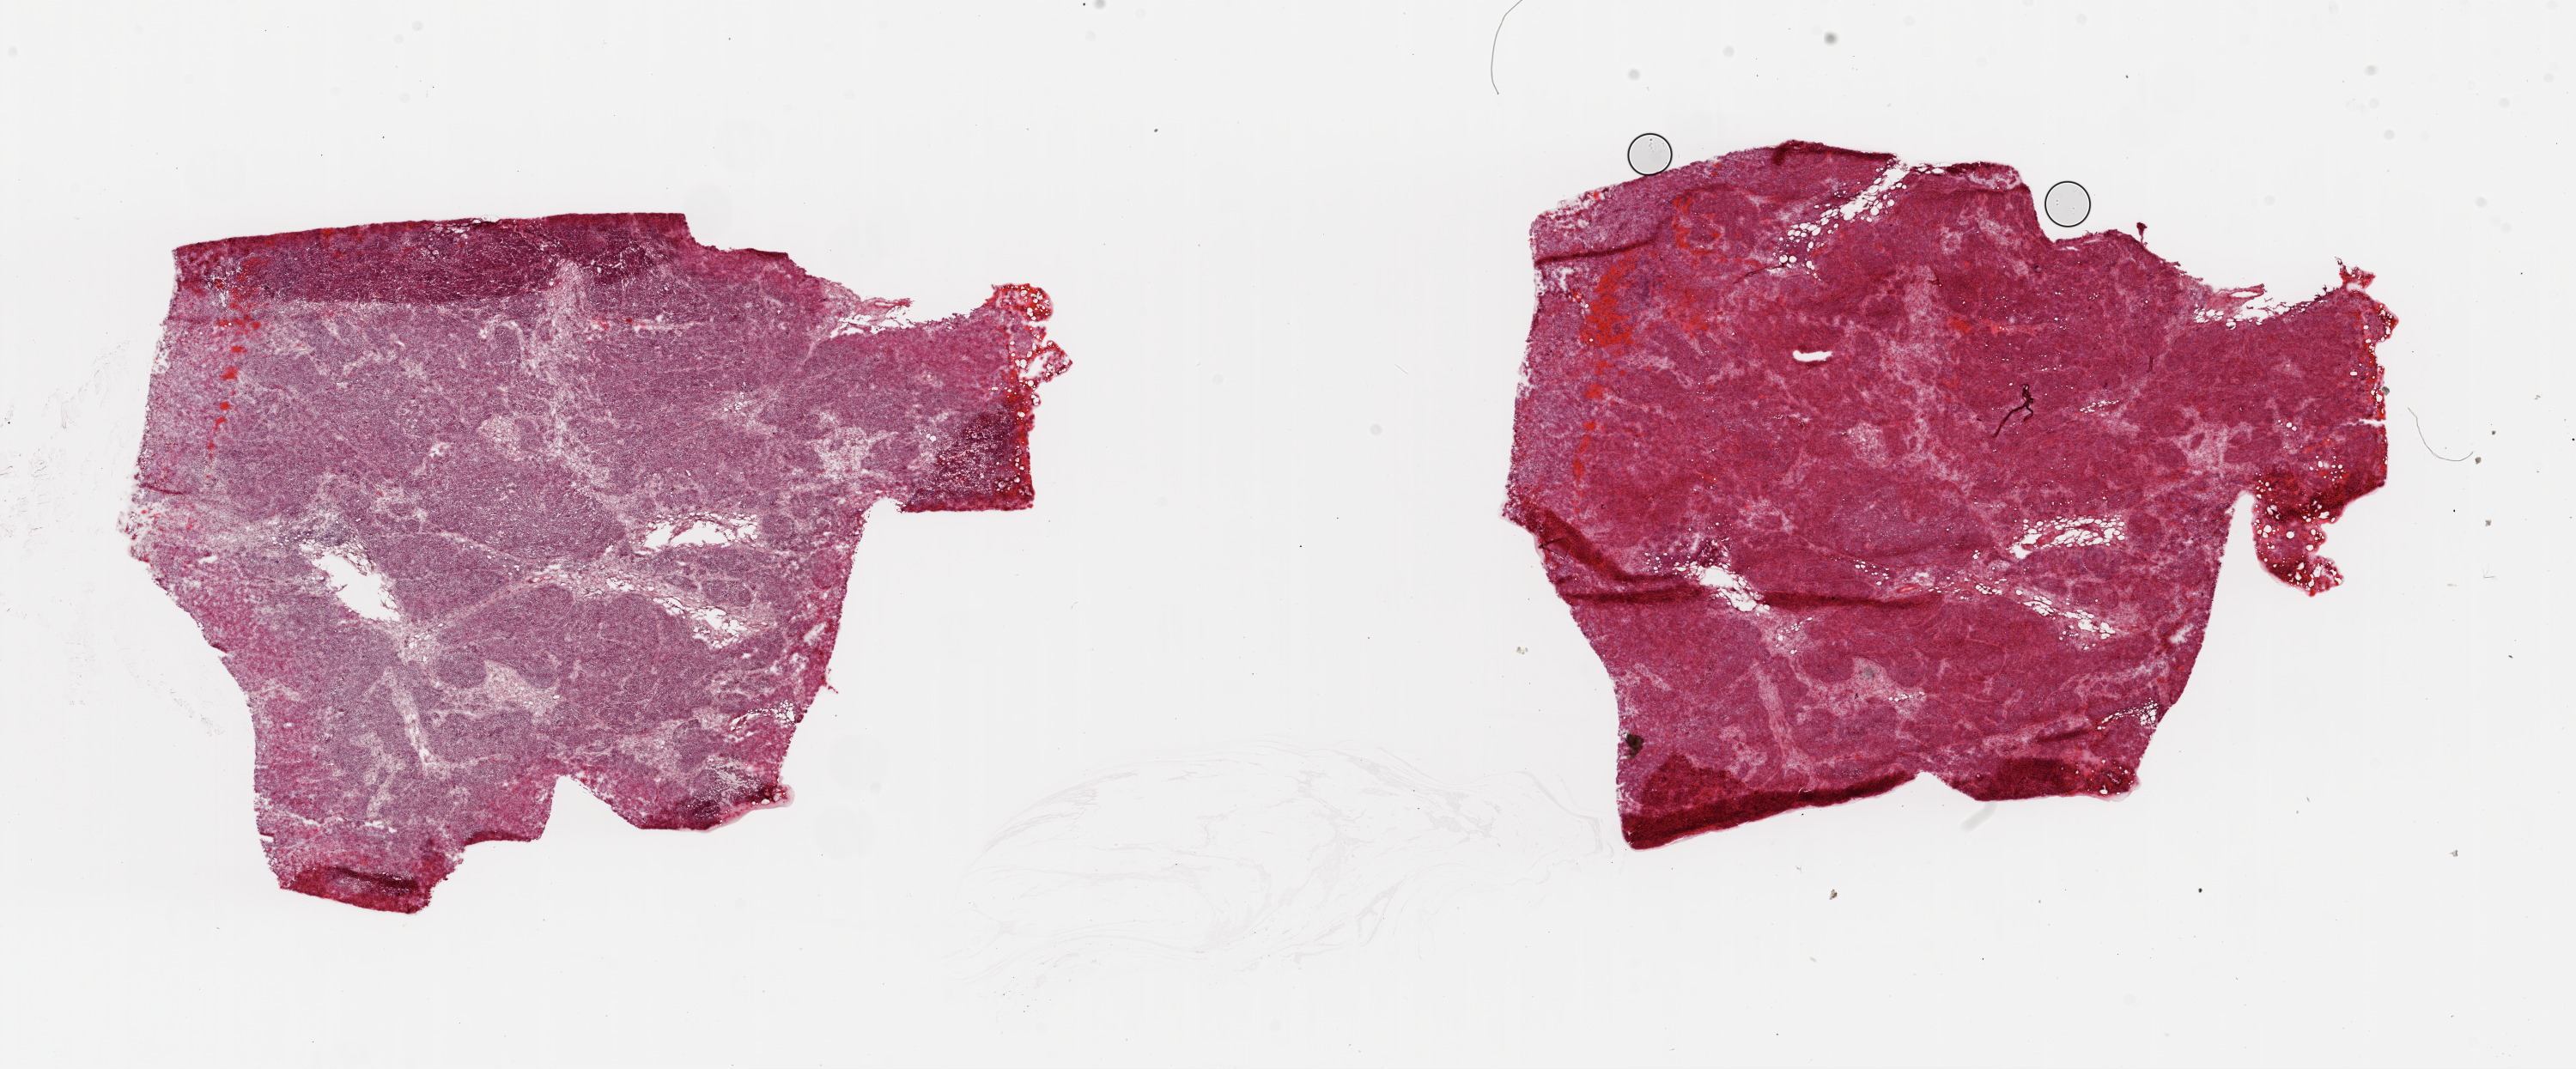
Whole-slide histology image, H&E — whole scanned area (about 24.1 x 10.0 mm) shown as a low-resolution overview; frozen section from the top of the tissue portion; sample: primary tumour, ovary. Female patient; age at initial diagnosis 54 years. Histologic grade: G3 (poorly differentiated). Pathologist review of this section (percent, as recorded): tumour cells 75%, tumour nuclei 85%, normal cells 15%, stromal cells 0%, necrosis 10%.
Diagnosis: Serous cystadenocarcinoma, NOS. Laterality: left. FIGO stage: IV.